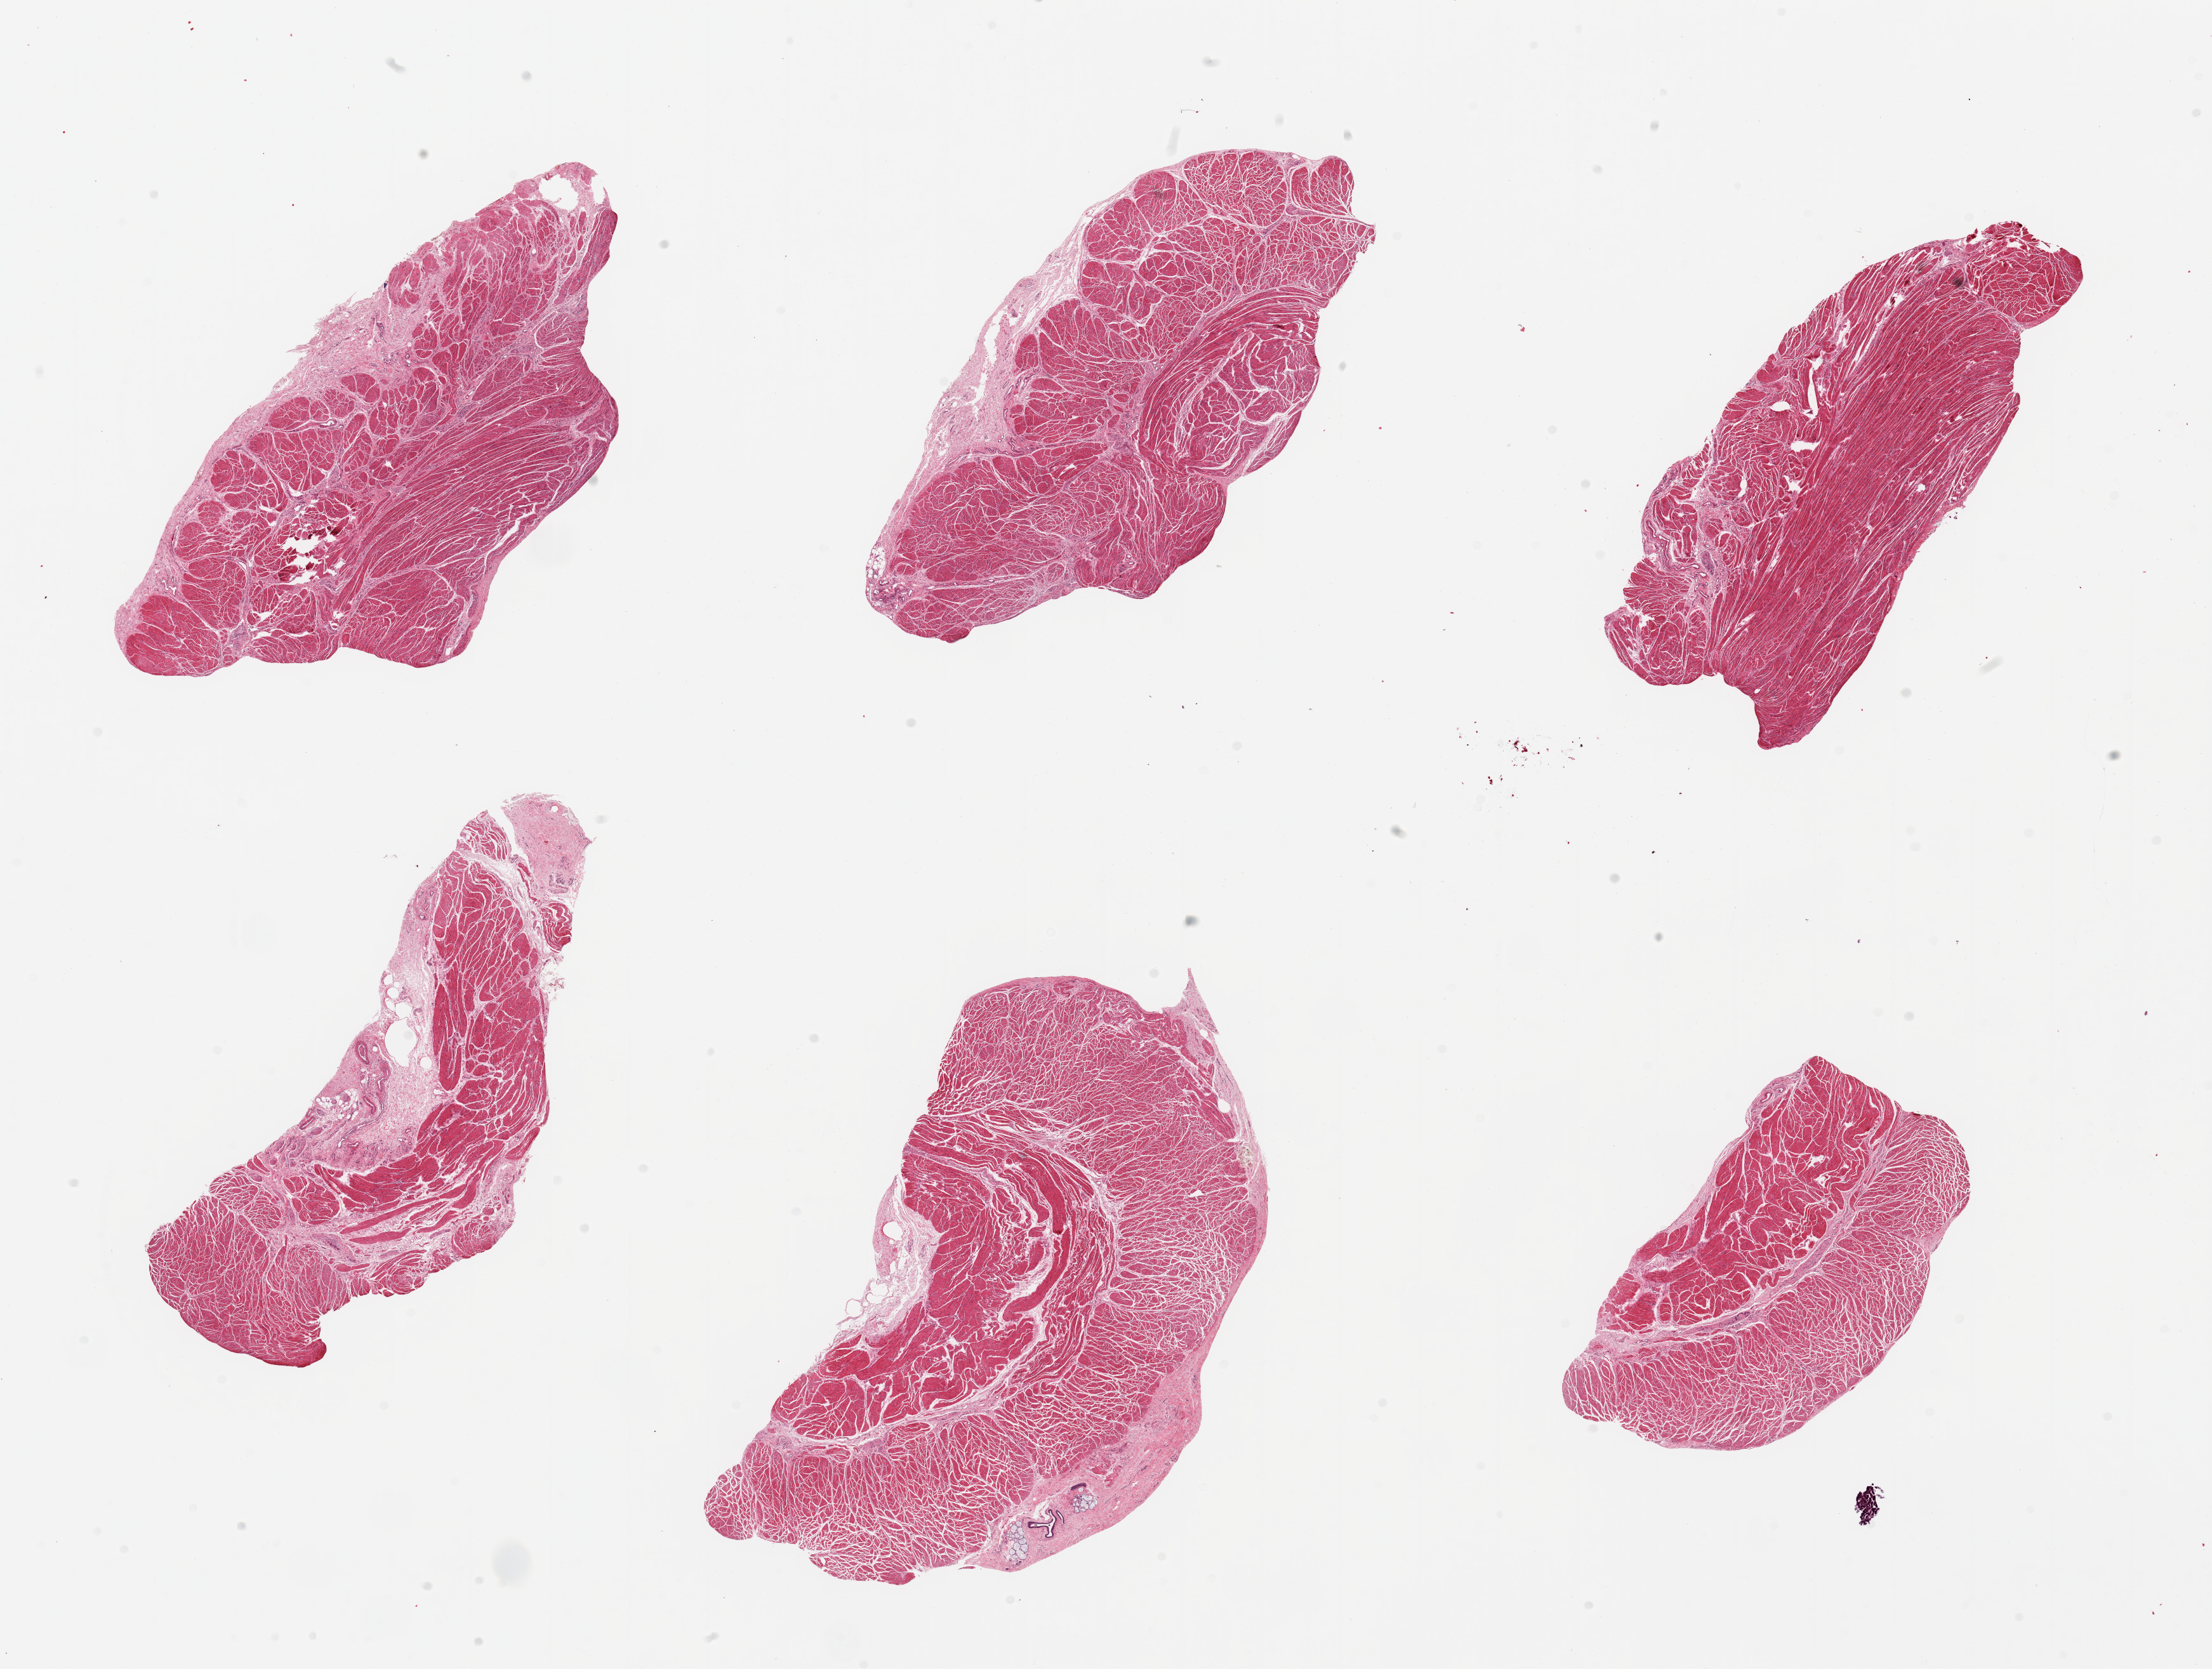
Hematoxylin and eosin (H&E) whole-slide image, brightfield — a low-resolution overview of the entire scanned area, about 27.6 x 20.8 mm (from a 20x scan), PAXgene-fixed paraffin-embedded (PFPE) section, sampled site (target tissue): esophageal muscle, donor tissue sample.
Pathologist's review note for this sample: 6 pieces, all muscularis.